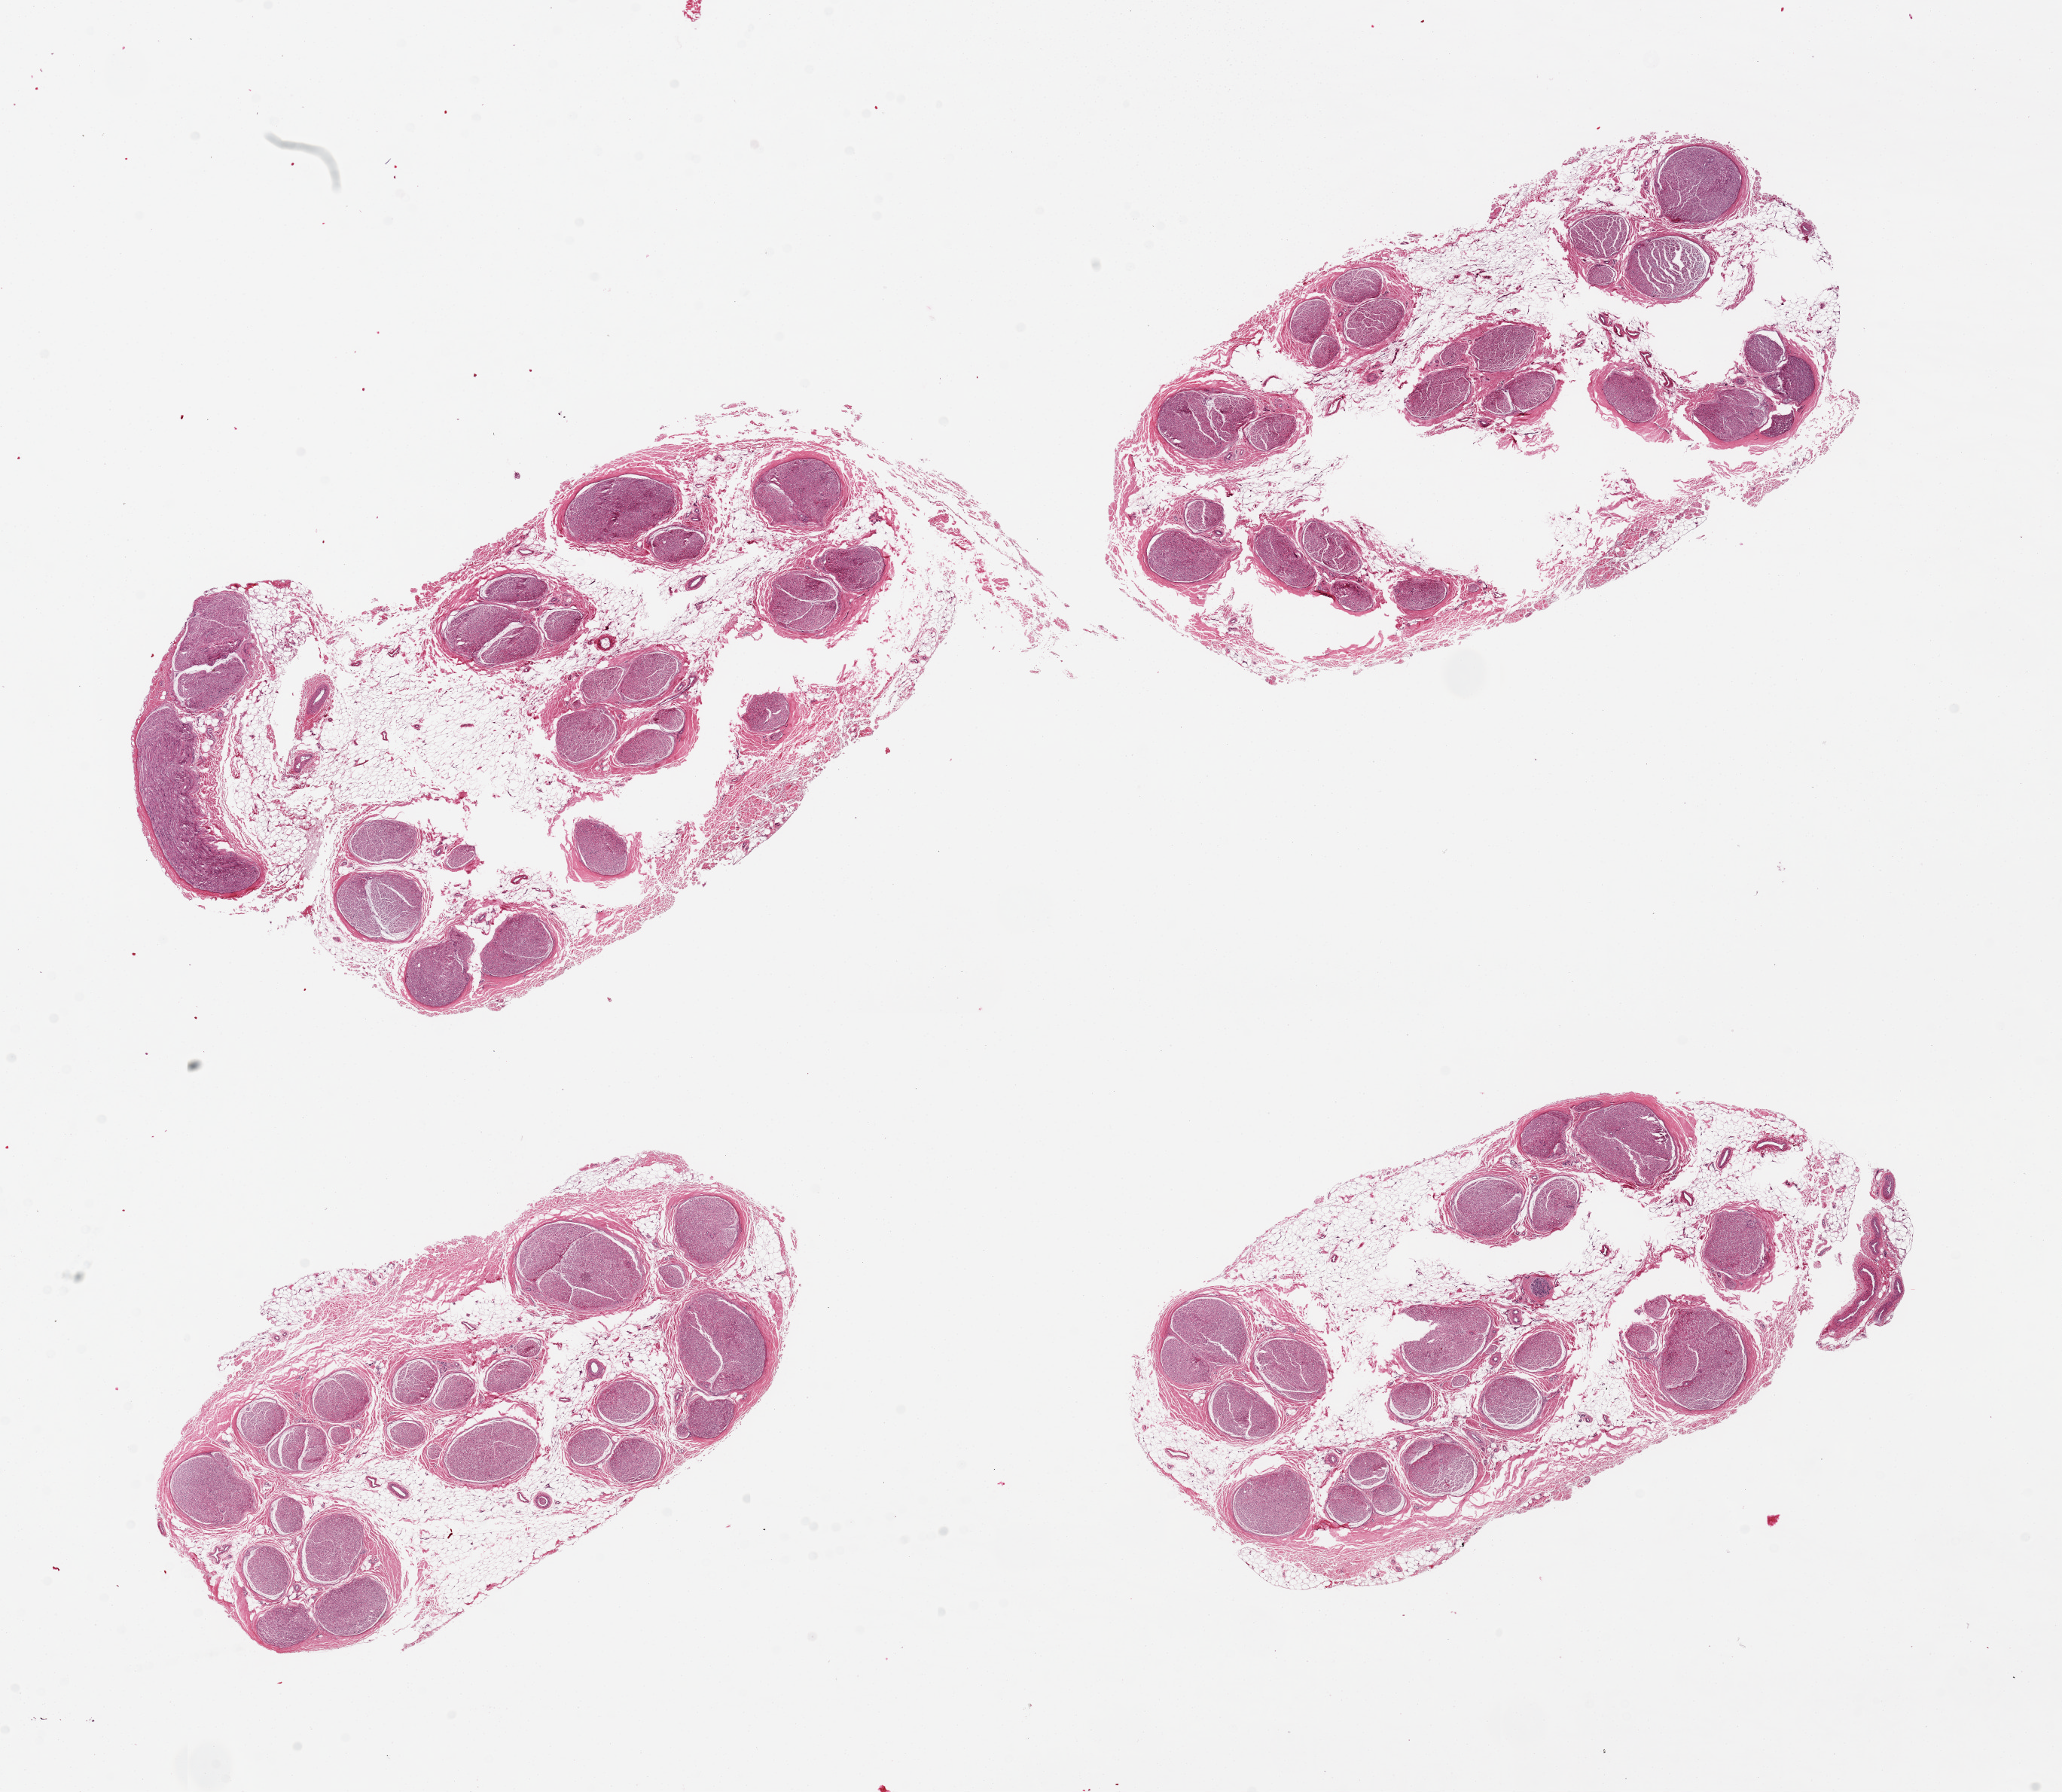
H&E whole-slide image, brightfield, whole scanned area (about 21.7 x 18.8 mm) shown as a low-resolution overview, PAXgene-fixed paraffin-embedded (PFPE) section, section of tibial nerve (target tissue), tissue donor sample.
Review note (as recorded): 4 pieces; approximately 30% internal and external fibroadipose tissue.